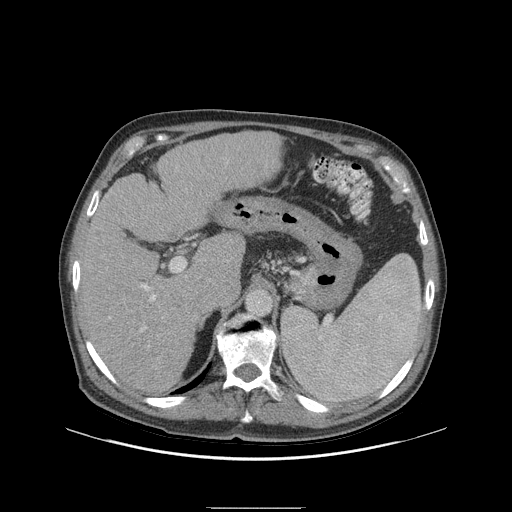
Contrast-enhanced abdominal CT (liver protocol), one axial slice. Slice 60 of 105 in the series (ordered by position). Reconstruction kernel STANDARD. Soft-tissue window (W 400 / L 40 HU). 2.5 mm slice thickness. 512 × 512 image matrix, field of view 440 × 440 mm. Case-level facts recorded for this patient, not image findings: diagnosis: hepatocellular carcinoma (patient treated with transarterial chemoembolisation; whether this scan precedes or follows treatment is not stated here); TNM stage (as recorded): Stage-I; Child-Pugh class: A; tumour nodularity: uninodular; tumour size: 5.1 cm.
Annotated regions visible in this slice (semi-automatic segmentation, software-assisted and operator-edited):
- liver parenchyma outside the tumour (the mass and vessels are separate outlines, so this box may not span the whole liver): bounding box [x1, y1, x2, y2] px = [80, 134, 277, 392]
- liver vessels: [140, 284, 156, 332]